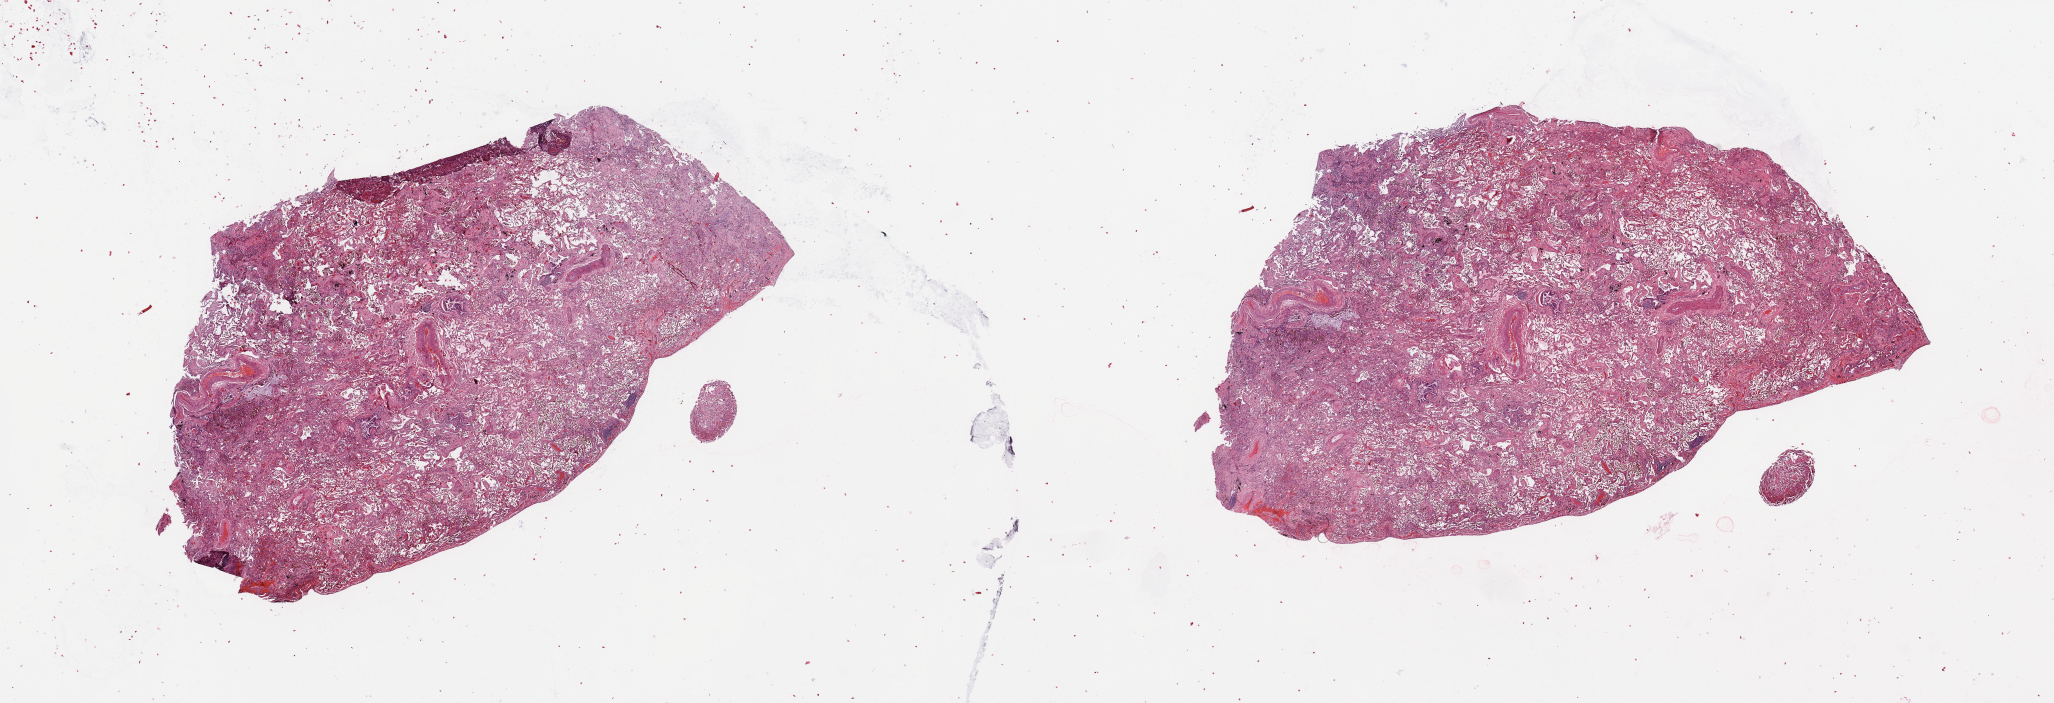
Digitized H&E-stained tissue section (whole slide) — whole scanned area (about 32.5 x 11.1 mm, acquisition: 20x scan) shown as a low-resolution overview, normal (non-tumour) tissue sample, sampled site: lung. 53-year-old male patient.
- this section: normal (non-tumour) tissue from the same patient
- patient diagnosis: Squamous cell carcinoma, NOS